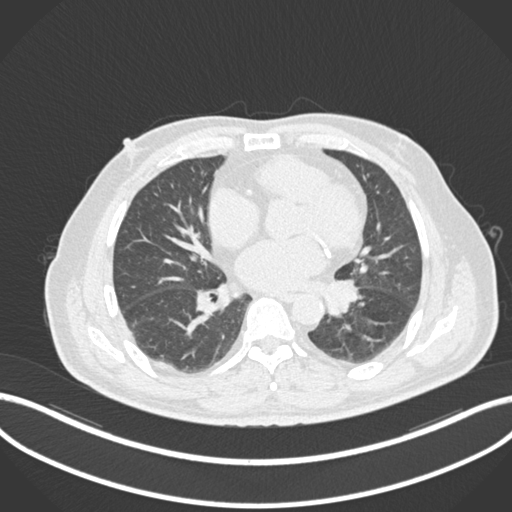
Chest CT, one axial slice. Slice 58 of 161 in the series (ordered by position). 120 kVp. Lung window (W 1500 / L -600 HU). 1 mm slice thickness. 512 × 512 image matrix, field of view 400 × 400 mm. Patient: male, 71 years. From the clinical record (not read from this slice): clinical TNM (as recorded): T1b N0 M0.
Annotated regions visible in this slice (bounding box drawn by a radiologist):
- lung tumour (recorded histology: squamous cell carcinoma): box from (x=324, y=274) to (x=363, y=320) px